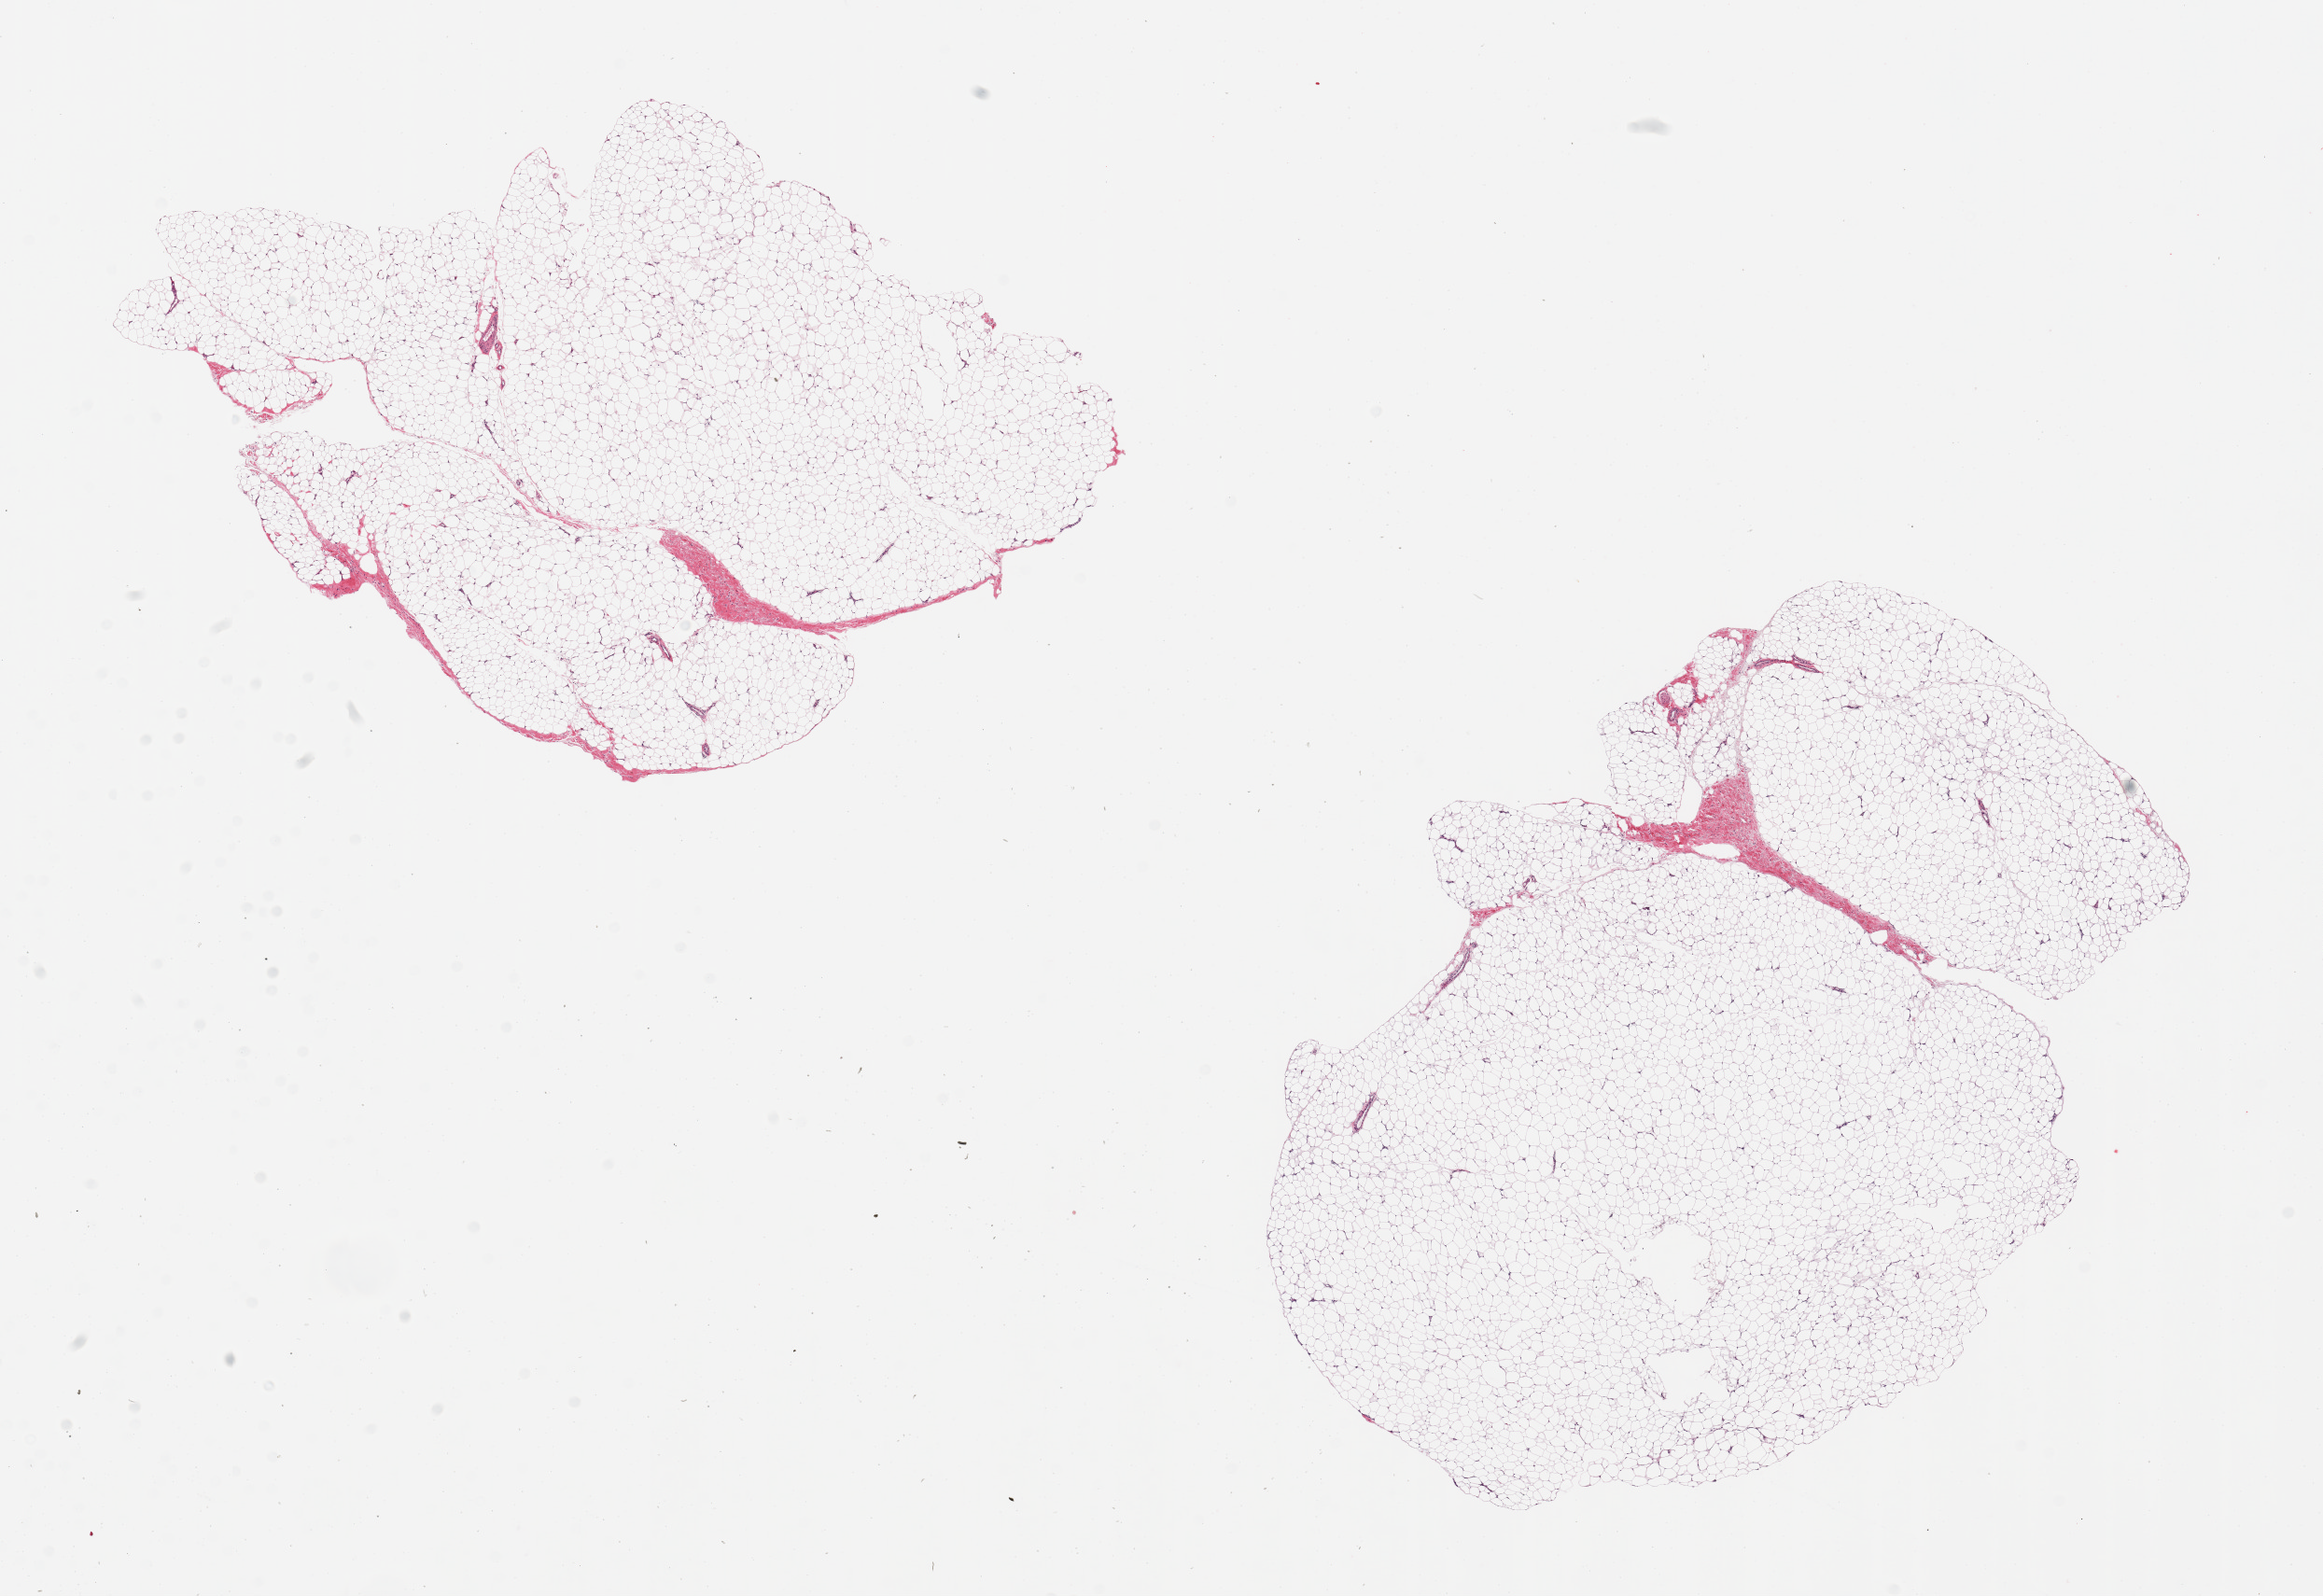
H&E whole-slide image, shown as a low-resolution overview of the whole scanned area (about 19.7 x 13.5 mm, from a 20x scan); PAXgene-fixed, paraffin-embedded tissue; section of adipose tissue (target tissue); tissue donor sample. Donor sex: male.
• reviewer comment on this tissue sample: 2 pieces, trace fascia, ~10%